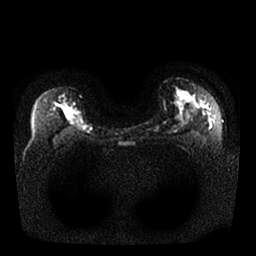
Breast MRI, one axial slice; slice 18 of 25 in the series (ordered by position); diffusion-weighted series; image 2 of 4 stored at this slice position (different b-values; order by instance number); 1.5 T; 4 mm slice thickness; 256 × 256 image matrix, field of view 340 × 340 mm. Female patient.
Structures marked on this image (outlined manually by an expert reader):
- tumour on diffusion-weighted imaging: bounding box (x1, y1, x2, y2) in pixels: (62, 105, 78, 120)